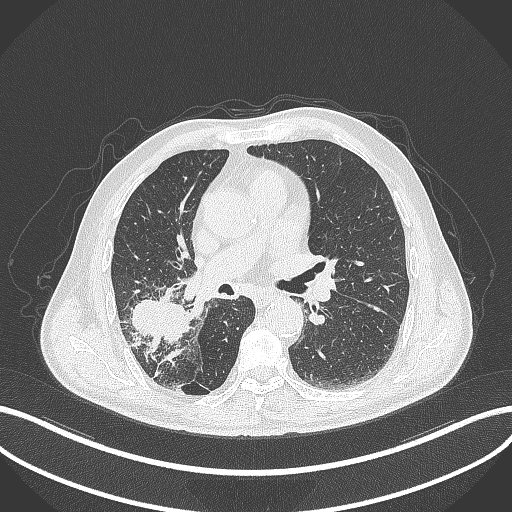
Chest CT, one axial slice; position 230 of 429 along the scan axis; lung window (W 1500 / L -600 HU); 512 × 512 image matrix. Patient: male, 72 years. Case-level facts recorded for this patient, not image findings: clinical TNM (as recorded): T3 N2 M0.
Annotated regions visible in this slice (bounding box drawn by a radiologist):
- lung tumour (recorded histology: adenocarcinoma): bounding box (x1, y1, x2, y2) in pixels: (125, 295, 191, 344)